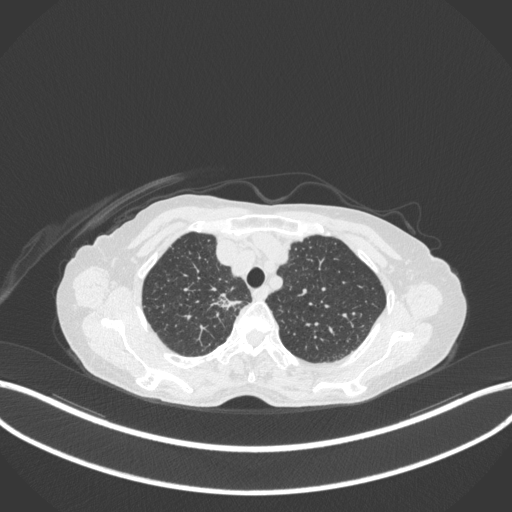
Chest CT, one axial slice. Slice 304 of 363 in the series (ordered by position). Lung window (W 1500 / L -600 HU). 1 mm slice thickness. 512 × 512 image matrix, field of view 400 × 400 mm. Female patient, age 75 years. From the clinical record (not read from this slice): clinical TNM (as recorded): T1c N1 M1.
Structures marked on this image (bounding box drawn by a radiologist):
- lung tumour (recorded histology: adenocarcinoma): bounding box [x1, y1, x2, y2] px = [212, 289, 243, 311]